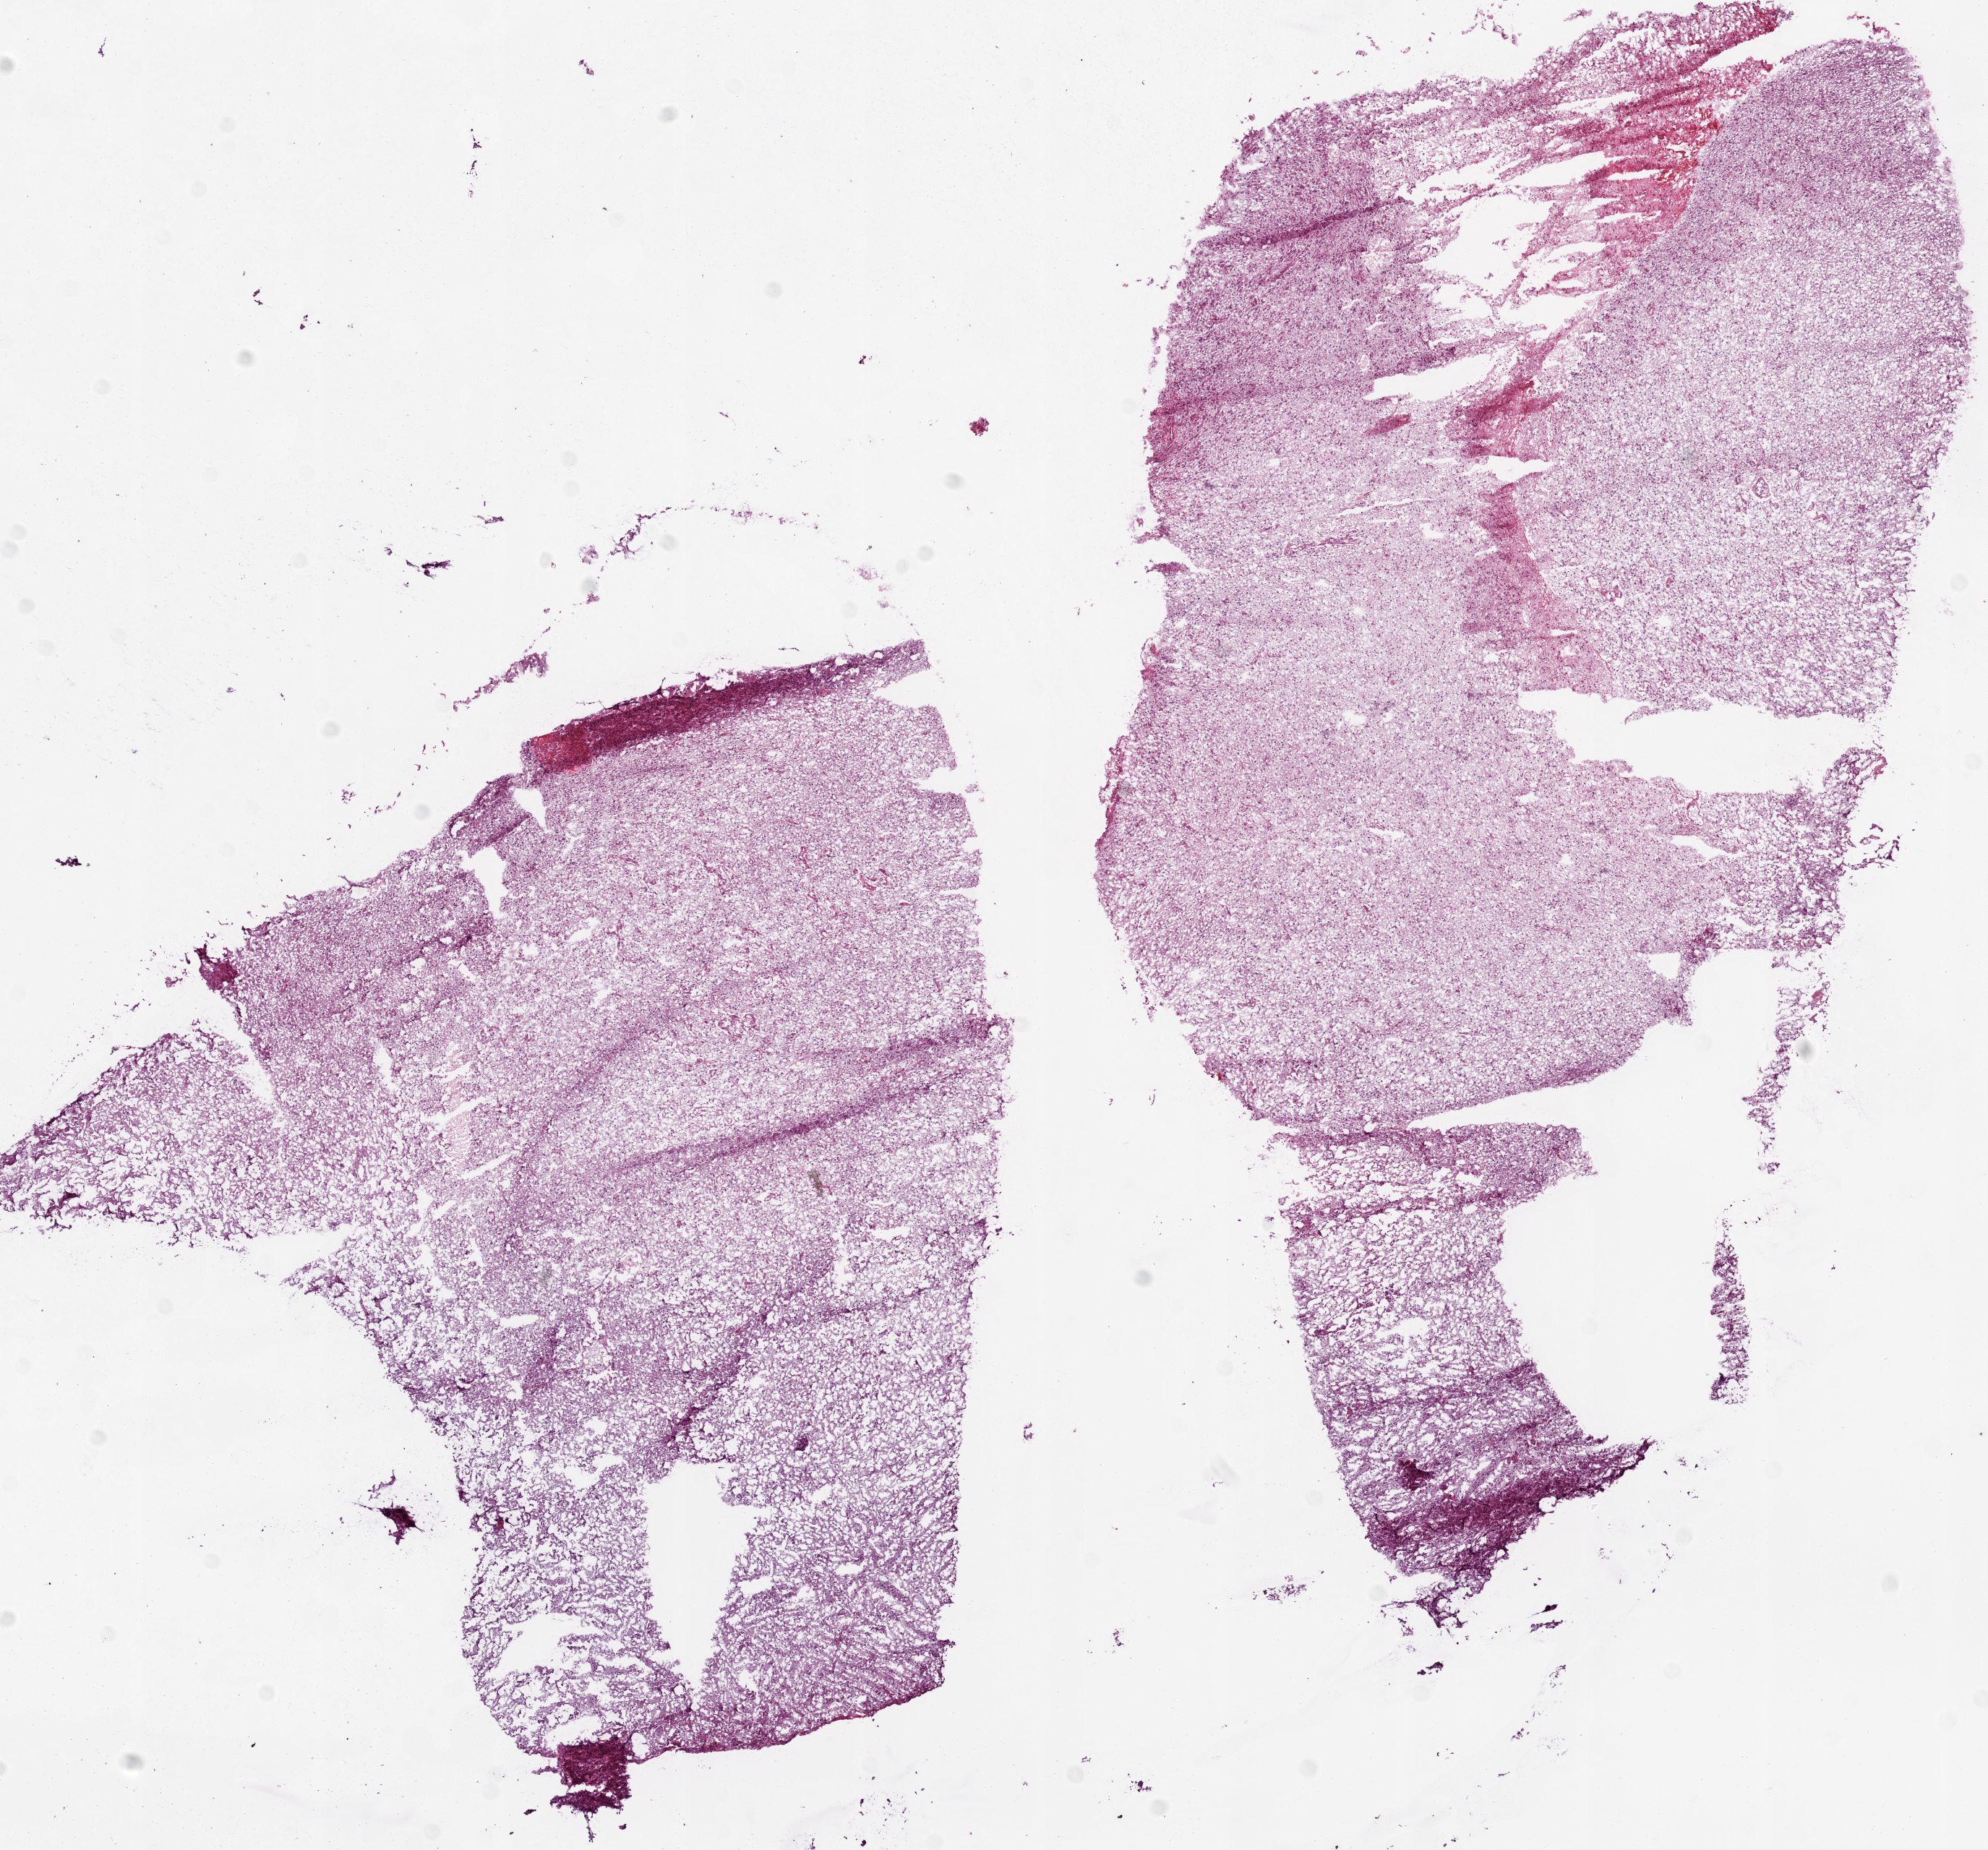
Whole-slide histology image, H&E, shown as a low-resolution overview of the whole scanned area (about 11.0 x 10.3 mm); frozen section from the bottom of the tissue portion; sample: primary tumour, brain. Male patient; age at initial diagnosis 55 years. Composition of this section per pathologist review: tumour cells 85%, tumour nuclei 100%, normal cells 0%, stromal cells 0%, necrosis 15%.
* histologic diagnosis: Glioblastoma